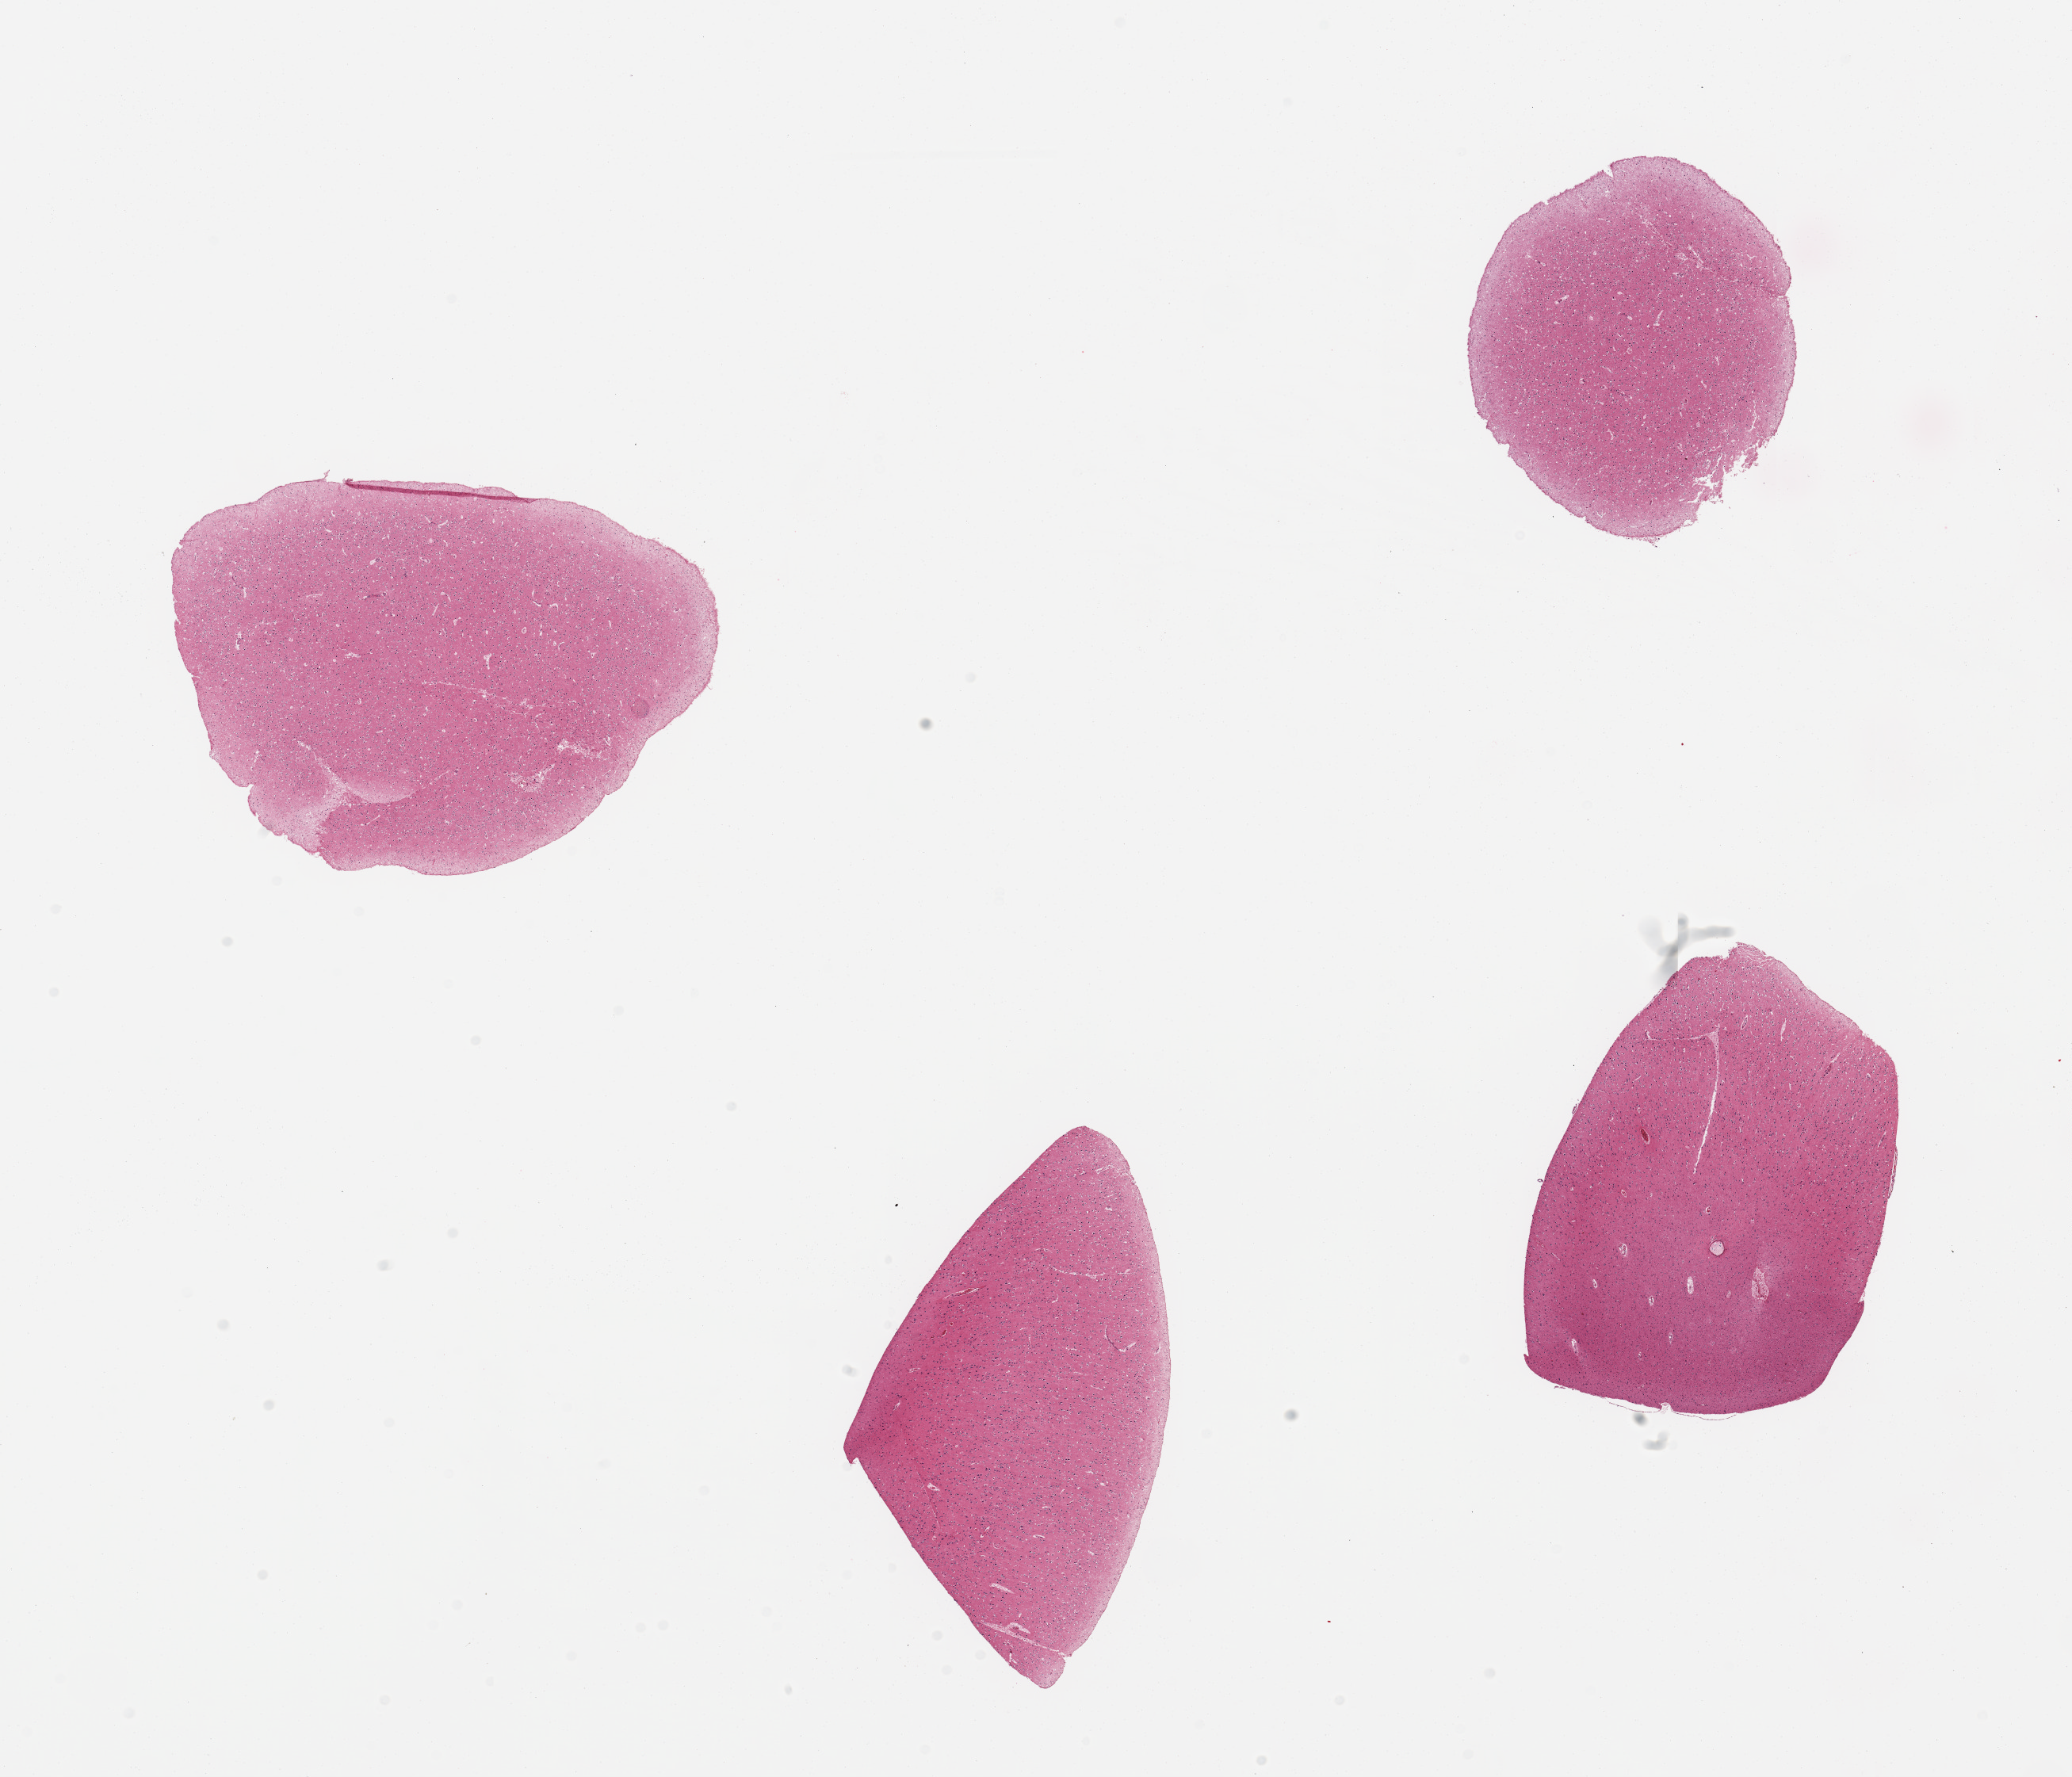
Whole-slide image, H&E stain, shown as a low-resolution overview of the whole scanned area (about 20.7 x 17.7 mm, acquisition: 20x scan). PAXgene-fixed, paraffin-embedded tissue. Sampled site (target tissue): cerebral cortex. Tissue donor sample. Donor sex: female.
Pathologist's review note for this sample: 4 pieces, no abnormalities.